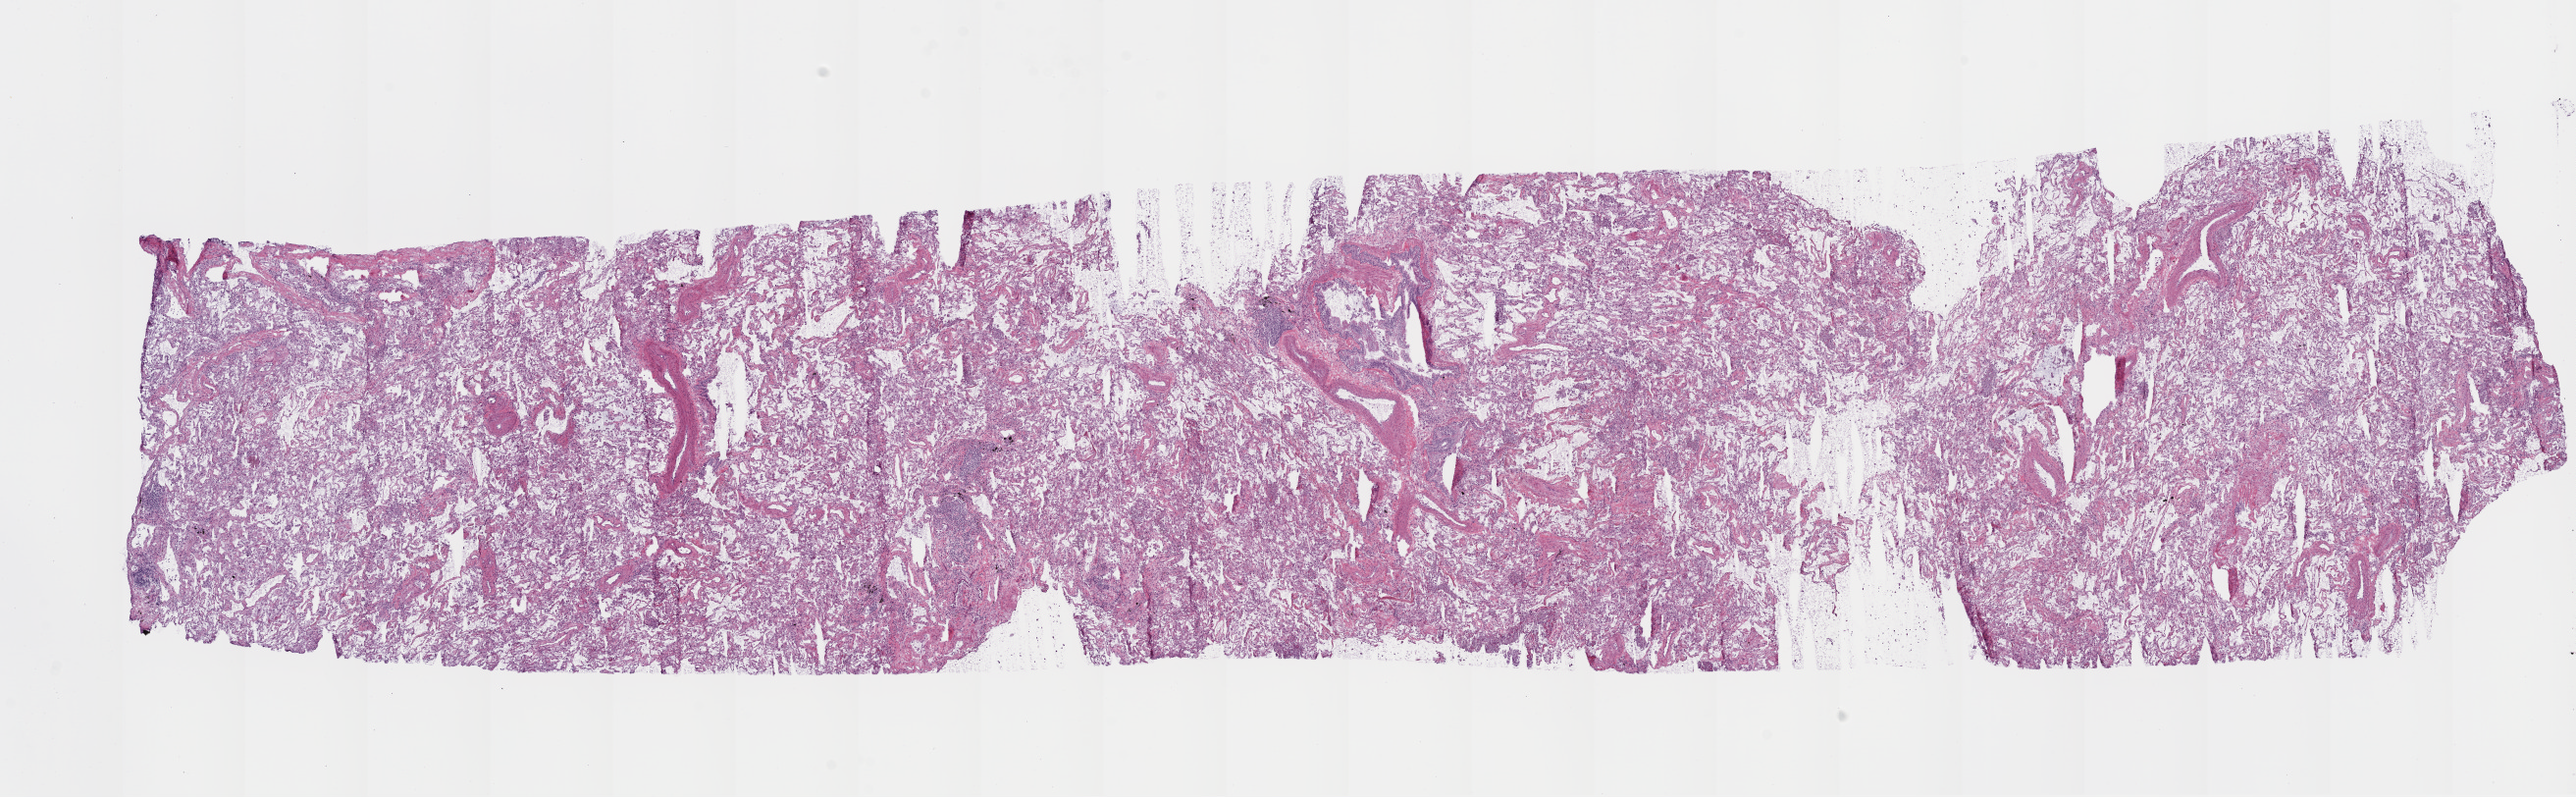
Whole-slide histology image, Hematoxylin and eosin (H&E) stained — shown as a low-resolution overview of the whole scanned area (about 21.1 x 6.5 mm); frozen section from the top of the tissue portion; solid tissue normal (non-tumour tissue) sample from the lung. Female, age 74 years at initial diagnosis.
* this section: solid tissue normal (non-tumour) sample from the same patient
* patient diagnosis: Adenocarcinoma, NOS (upper lobe, lung)